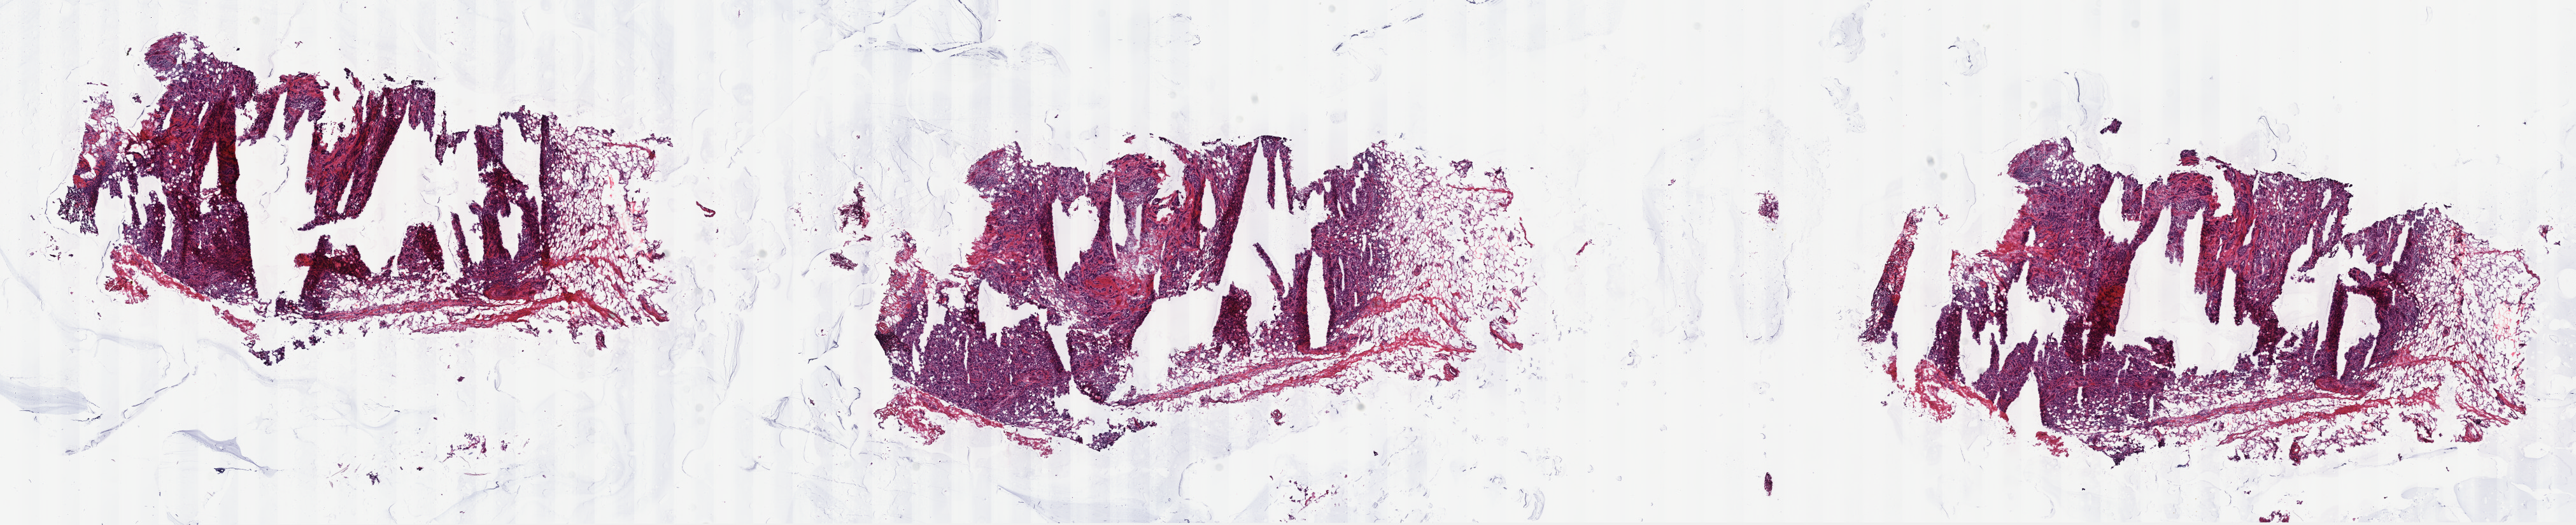
Hematoxylin and eosin (H&E) stained whole-slide image, shown as a low-resolution overview of the whole scanned area (about 32.7 x 6.7 mm, acquisition: 40x scan), frozen section, sample: primary tumour, breast. Female, age 72 years at initial diagnosis. Pathologist review of this section (percent, as recorded): tumour cells 45%, tumour nuclei 82%.
Diagnosis: Infiltrating duct carcinoma, NOS.